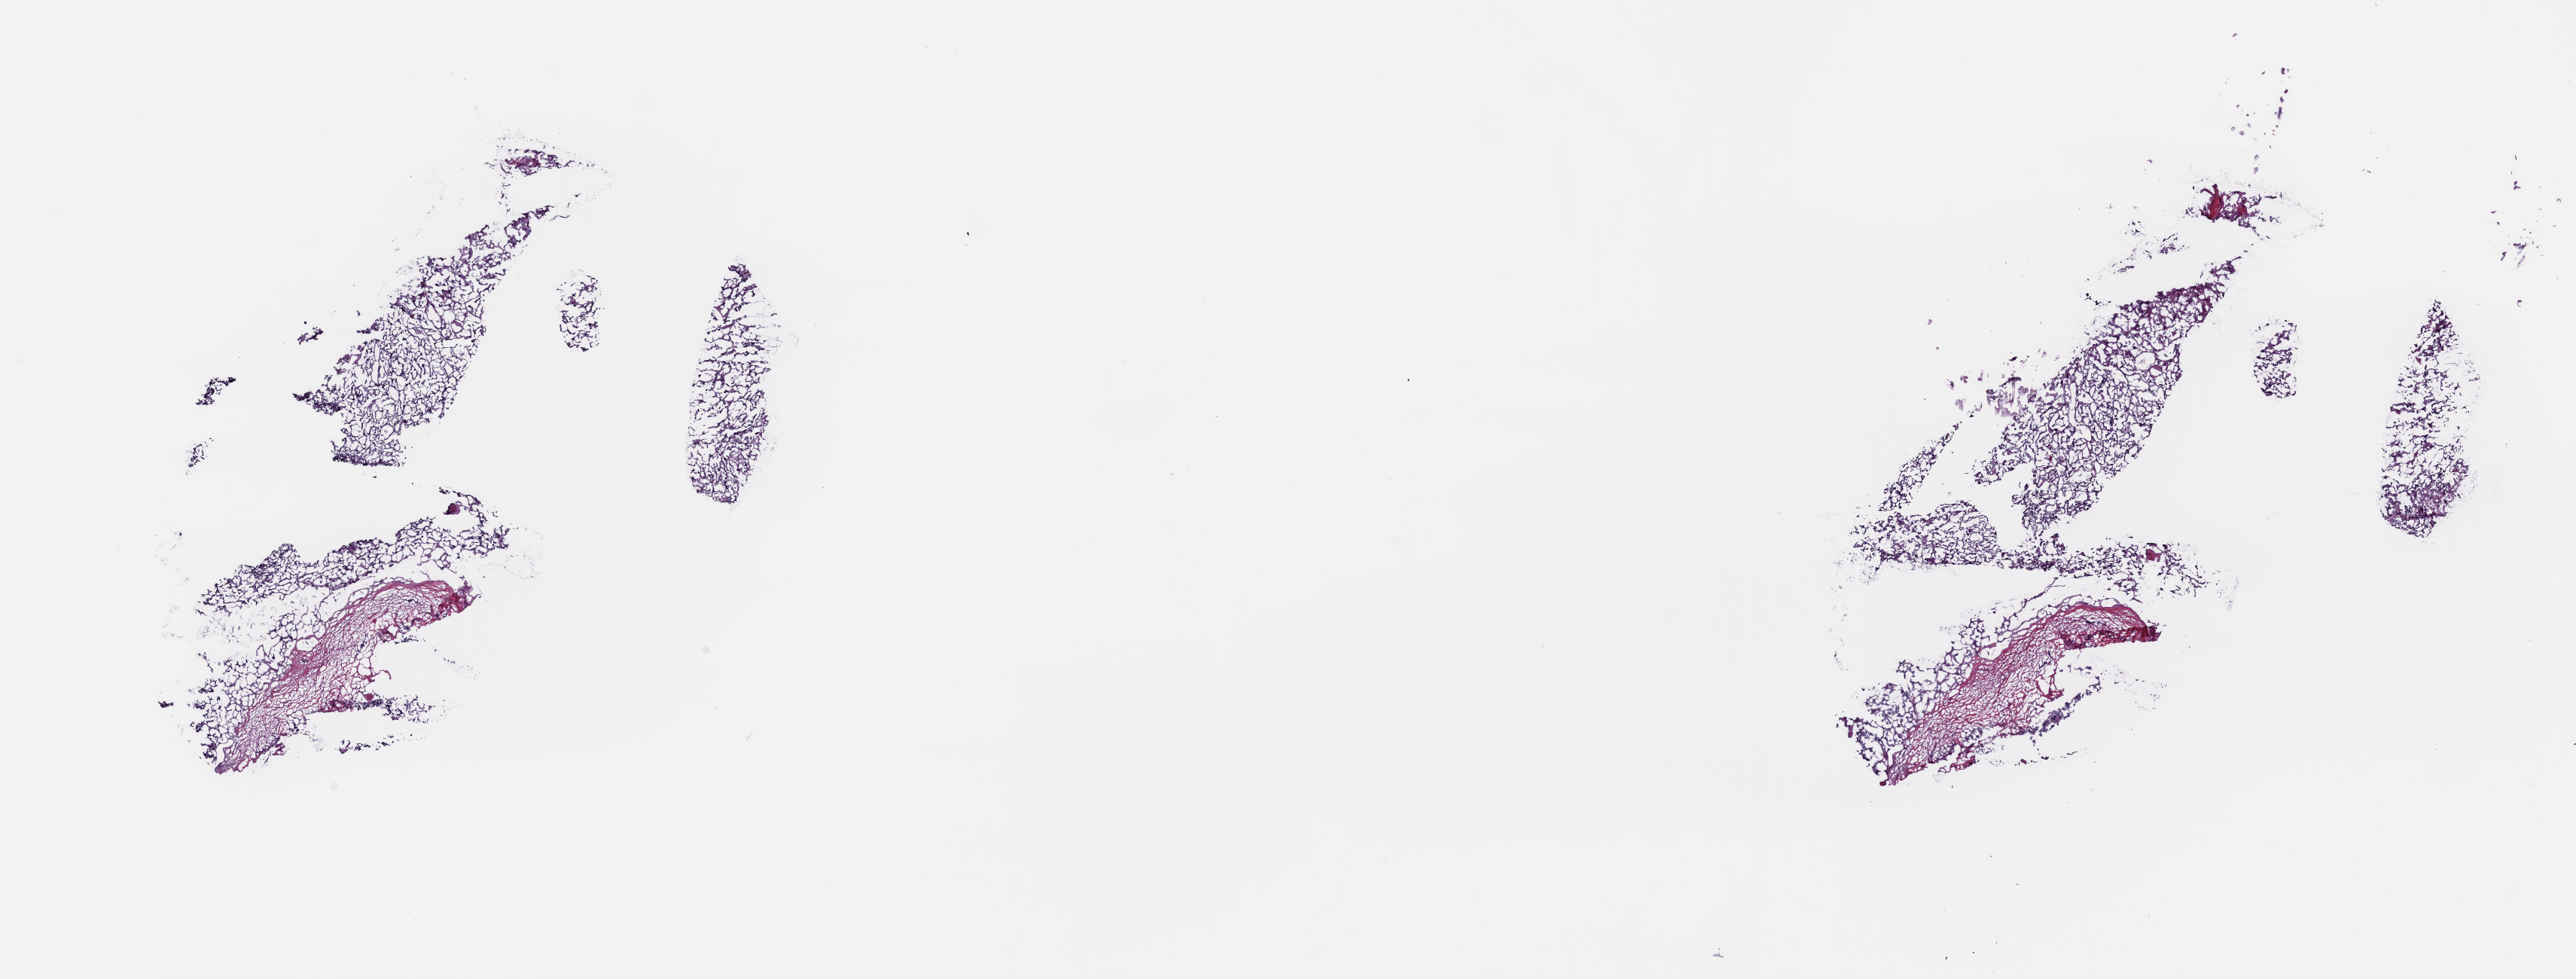
H&E-stained whole-slide image — whole scanned area (about 27.0 x 10.3 mm, slide scanned at 40x) shown as a low-resolution overview, frozen section from the top of the tissue portion, primary tumour sample from the thyroid. Female patient; age at initial diagnosis 72 years. Slide review estimates, as recorded: tumour cells 80%, tumour nuclei 100%, normal cells 0%, stromal cells 20%, necrosis 0%. Infiltration values recorded for this section: lymphocyte infiltration 0%, monocyte infiltration 0%, neutrophil infiltration 0%.
Lymph nodes positive (case pathology): 0 of 1 examined. TNM: T1 N0 M0. Histologic diagnosis: Papillary carcinoma, follicular variant (thyroid gland). AJCC pathologic stage: I (7th edition).